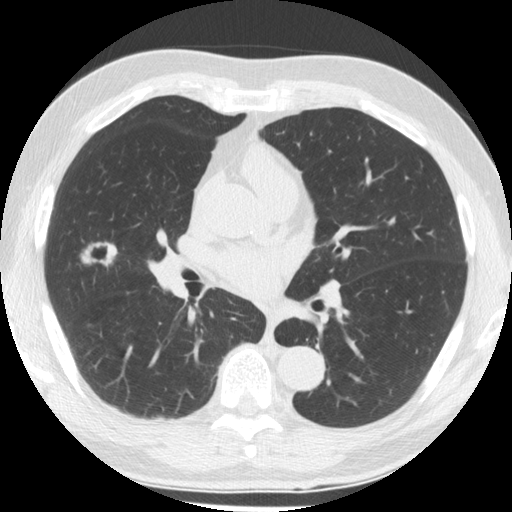
Chest CT (low-dose screening protocol), one axial image; first (baseline) screen; lung window (W 1500 / L -600 HU). Male, age 64 years at enrolment.
- Expert reader's lesion annotation, box from (x=62, y=221) to (x=128, y=285) px.
- The screening reader recorded 2 non-calcified nodules or masses ≥4 mm on this exam (right middle lobe, left lower lobe); which of them this box marks is not recorded.
- Participant outcome: lung cancer diagnosed 58 days after this screen — papillary adenocarcinoma, NOS, right middle lobe, well differentiated (G1), stage IA (AJCC 6th edition), 25 mm at pathology.